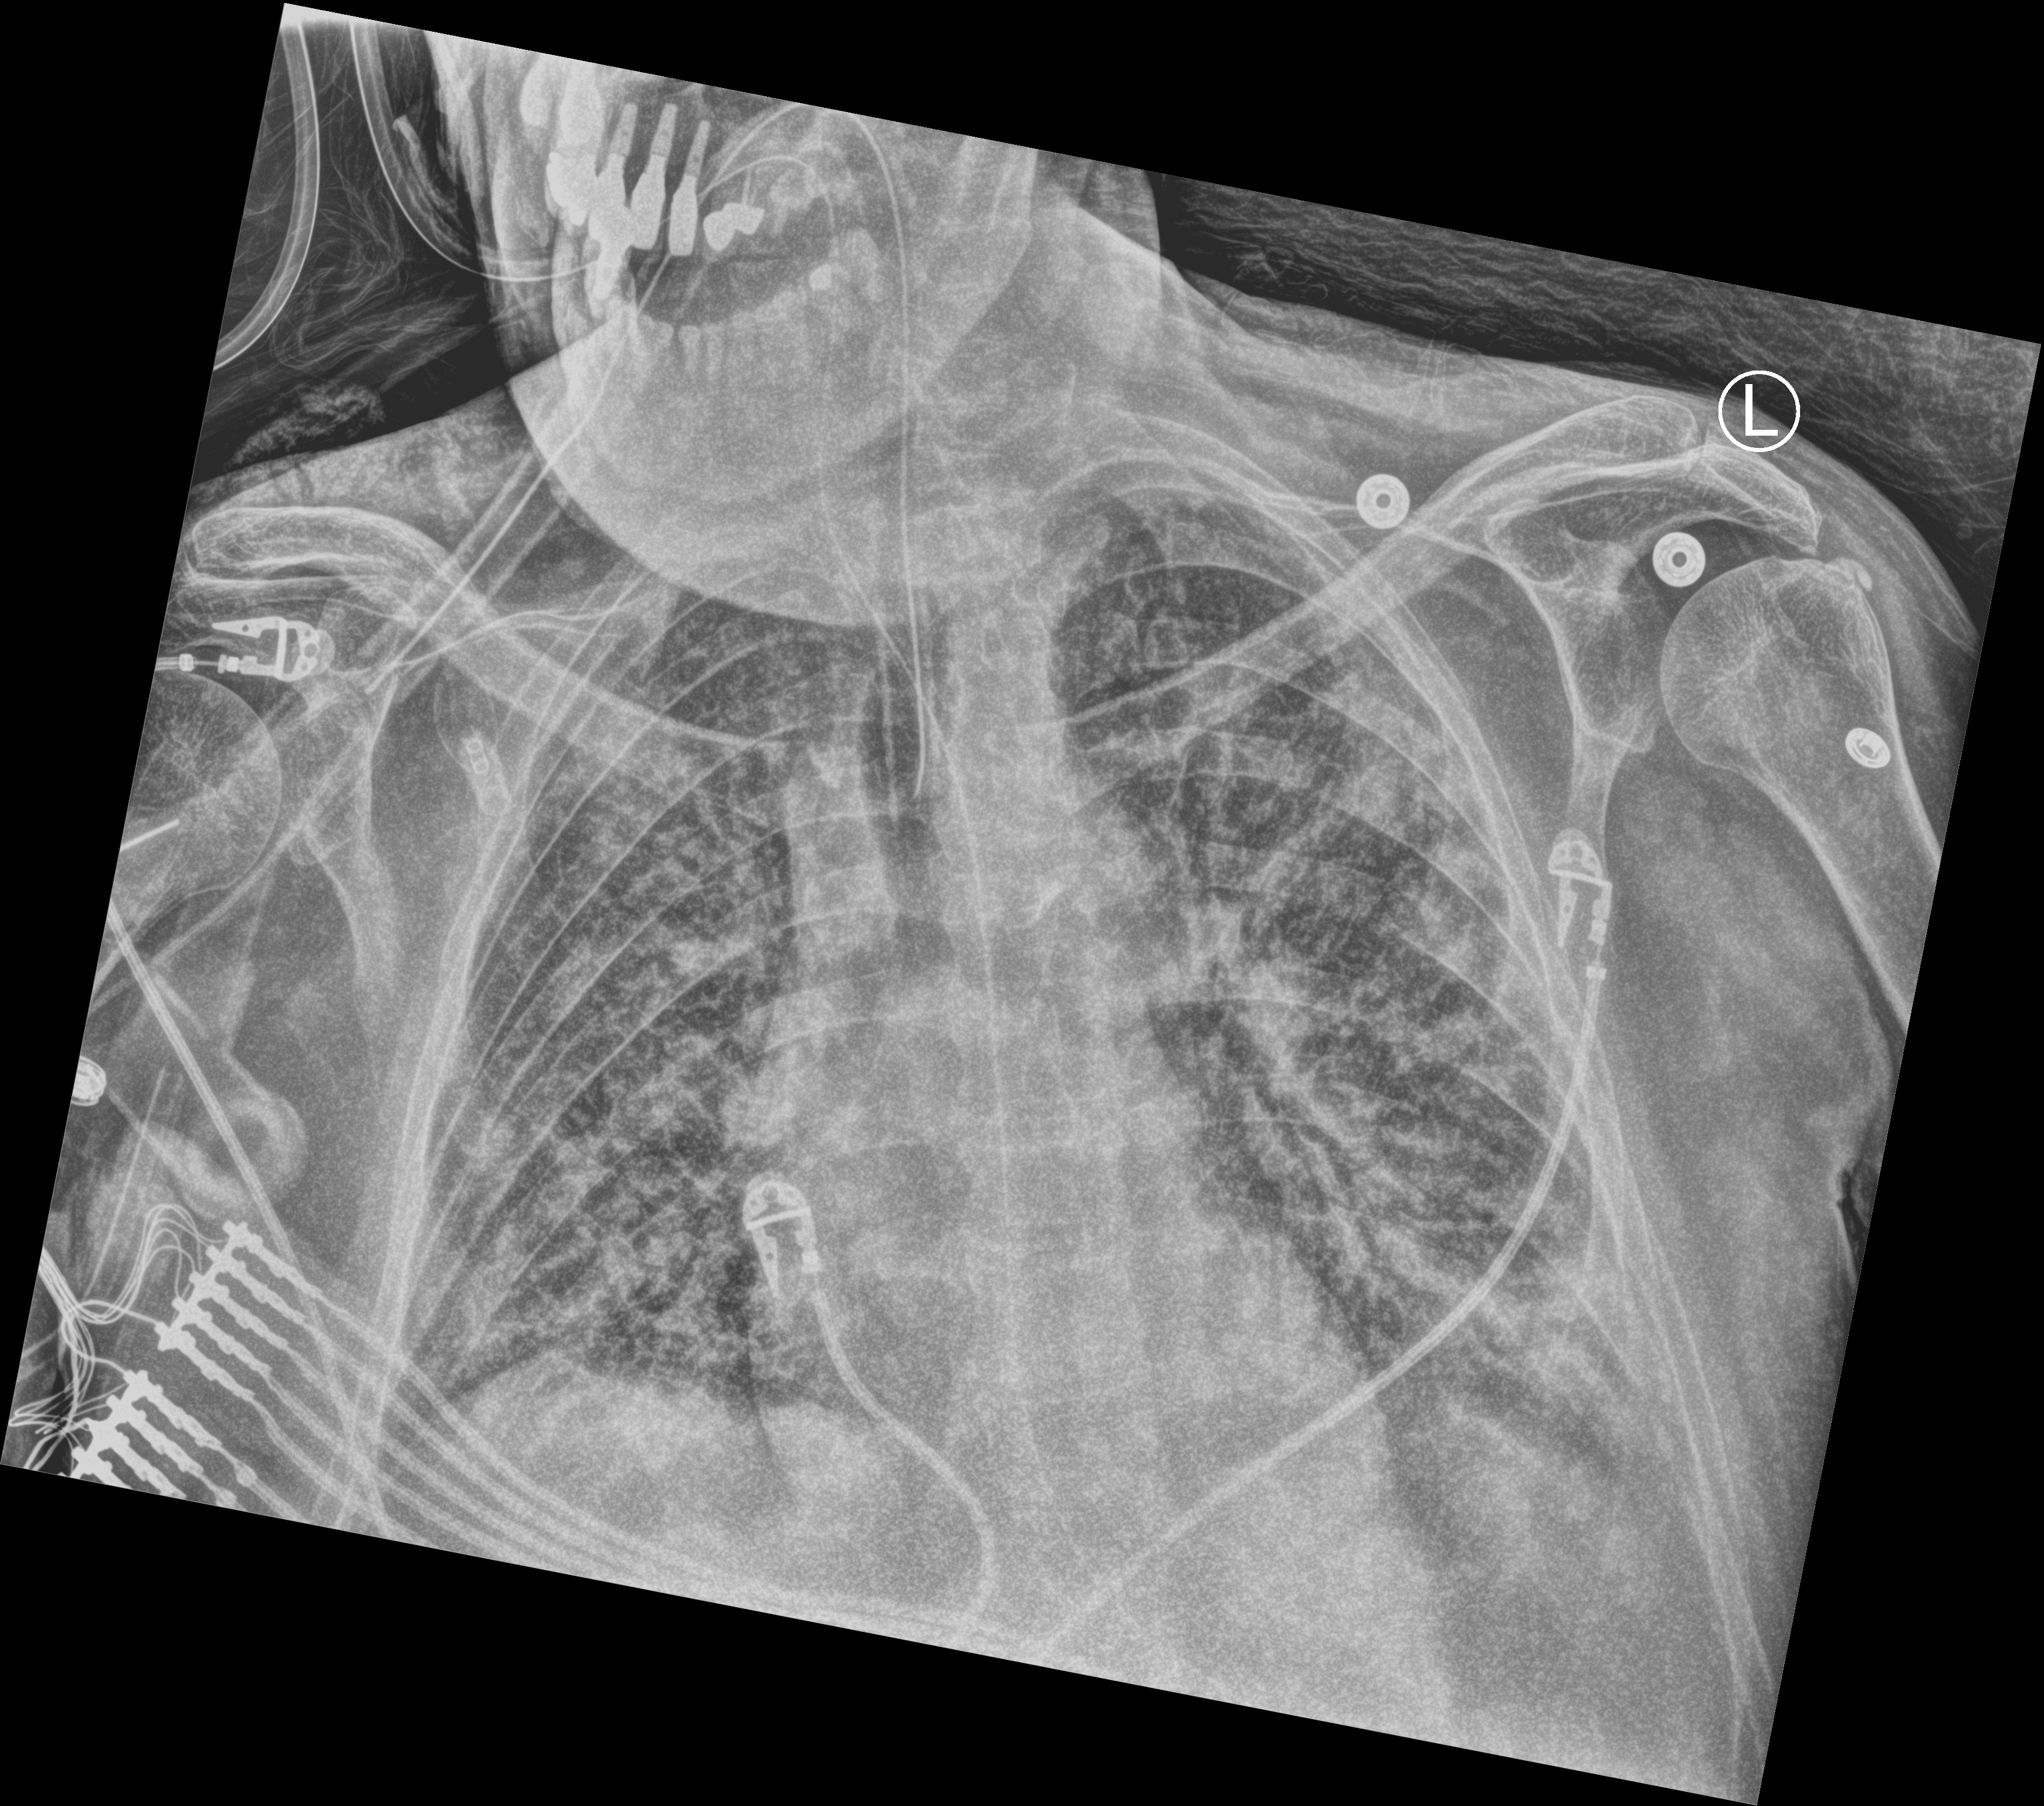
Chest X-ray (portable); anteroposterior (AP) projection. Patient hospitalised with COVID-19; male, aged 60–74 years.
Admission-level facts for this patient (not findings on this image; timing relative to this image not recorded): length of hospital stay: 25 days; other chronic lung disease (admission record): no; admitted to intensive care during this hospital stay: yes.